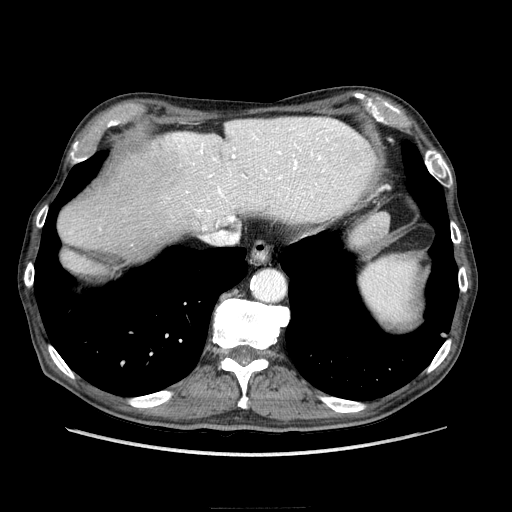
Contrast-enhanced abdominal CT (liver protocol), one axial slice. Slice 187 of 218 in the series (ordered by position). Reconstruction kernel STANDARD. 100 kVp. Soft-tissue window (W 400 / L 40 HU). 2.5 mm slice thickness. 512 × 512 image matrix, field of view 380 × 380 mm. Case-level facts recorded for this patient, not image findings: diagnosis: hepatocellular carcinoma (patient treated with transarterial chemoembolisation; whether this scan precedes or follows treatment is not stated here); TNM stage (as recorded): Stage-IIIA; Child-Pugh class: A; tumour differentiation: well differentiated; tumour size: 20 cm.
Outlined on this slice (semi-automatic segmentation, software-assisted and operator-edited):
- liver parenchyma outside the tumour (the mass and vessels are separate outlines, so this box may not span the whole liver): bounding box [x1, y1, x2, y2] px = [114, 118, 374, 260]
- liver vessels: [167, 118, 366, 230]